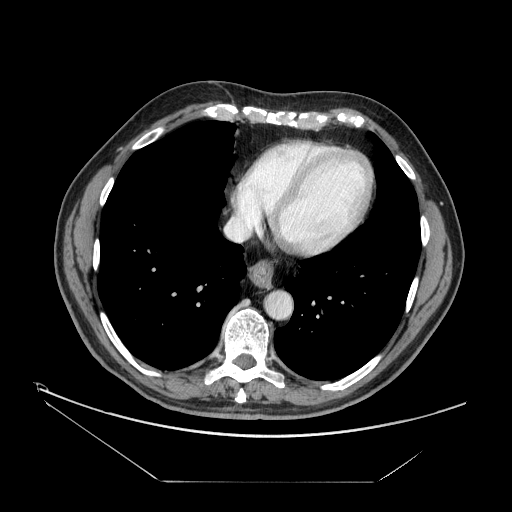
Contrast-enhanced abdominal CT, one axial slice; slice 158 of 161 in the series (ordered by position); 120 kVp; intravenous contrast given; soft-tissue window (W 400 / L 40 HU); 2.5 mm slice thickness; 512 × 512 image matrix. Male patient, age 65 years. Case-level facts recorded for this patient, not image findings: diagnosis: colorectal cancer liver metastases, imaged before liver resection; multiple liver metastases: yes; largest metastasis: 4.2 cm; disease in both lobes: yes.
Structures marked on this image (outlined manually by an expert reader):
- hepatic veins: bounding box (x1, y1, x2, y2) in pixels: (225, 162, 266, 240)